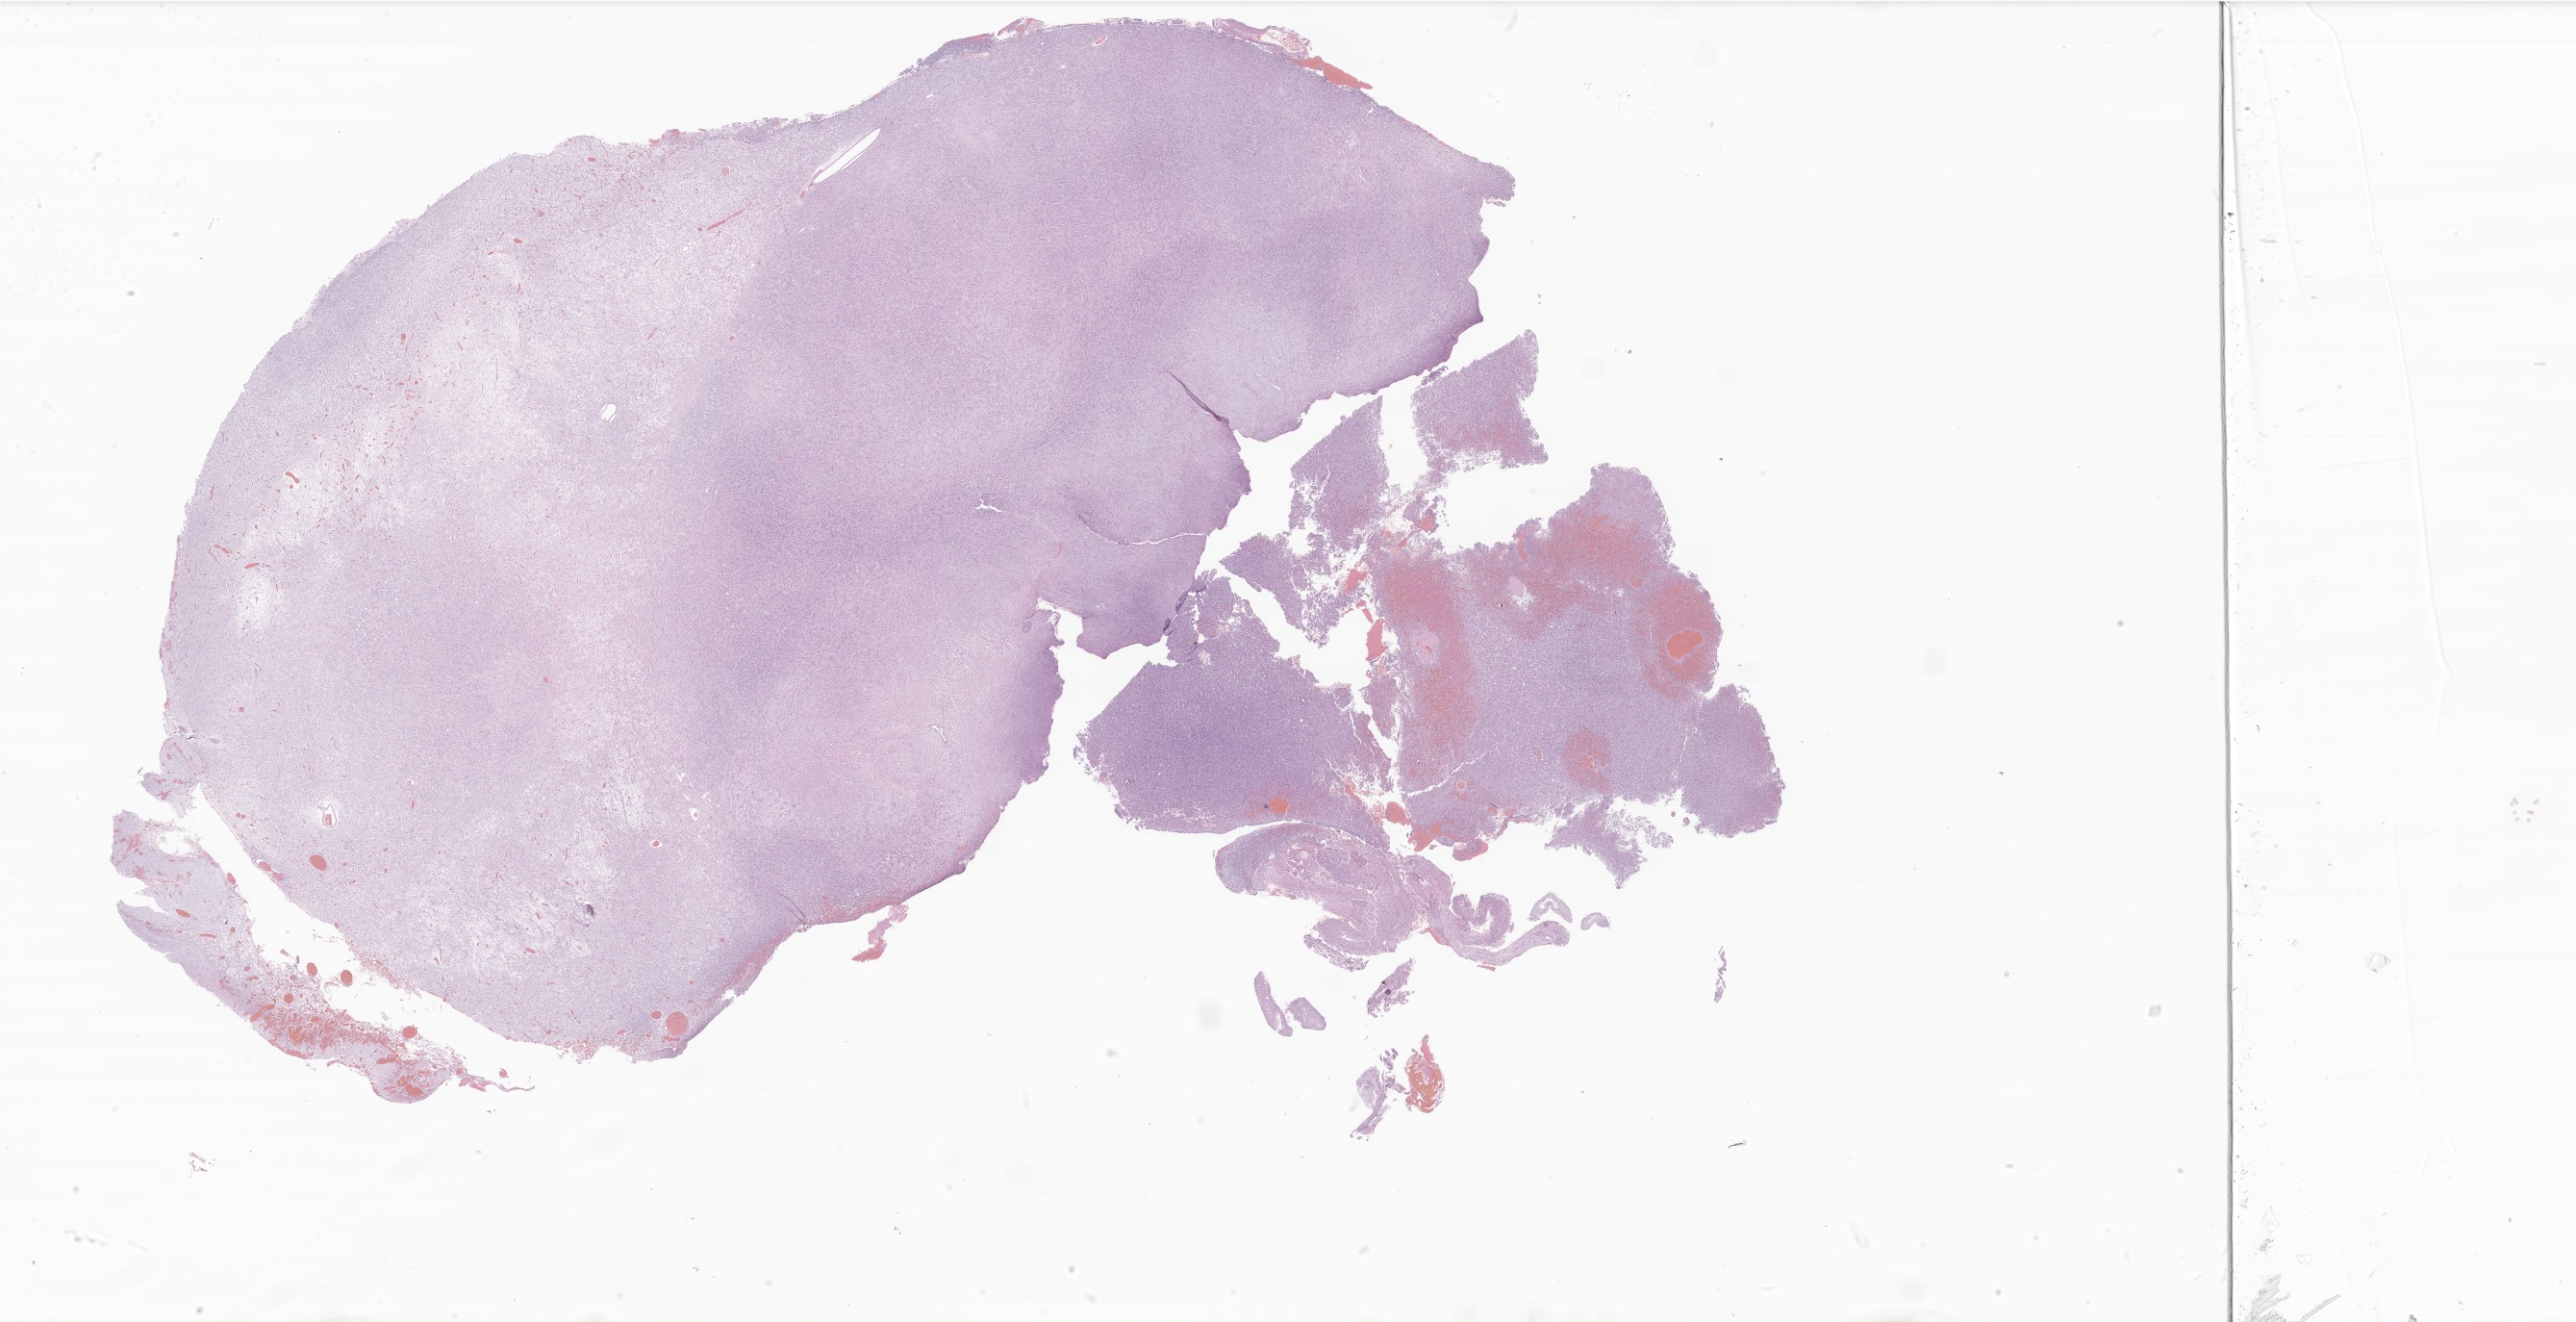
Digitized H&E-stained section of tumor tissue from the brain, a low-resolution overview of the entire scanned area, about 45.2 x 23.2 mm, FFPE section. Male patient, age 283 days.
Recorded diagnosis: Glioma, malignant.